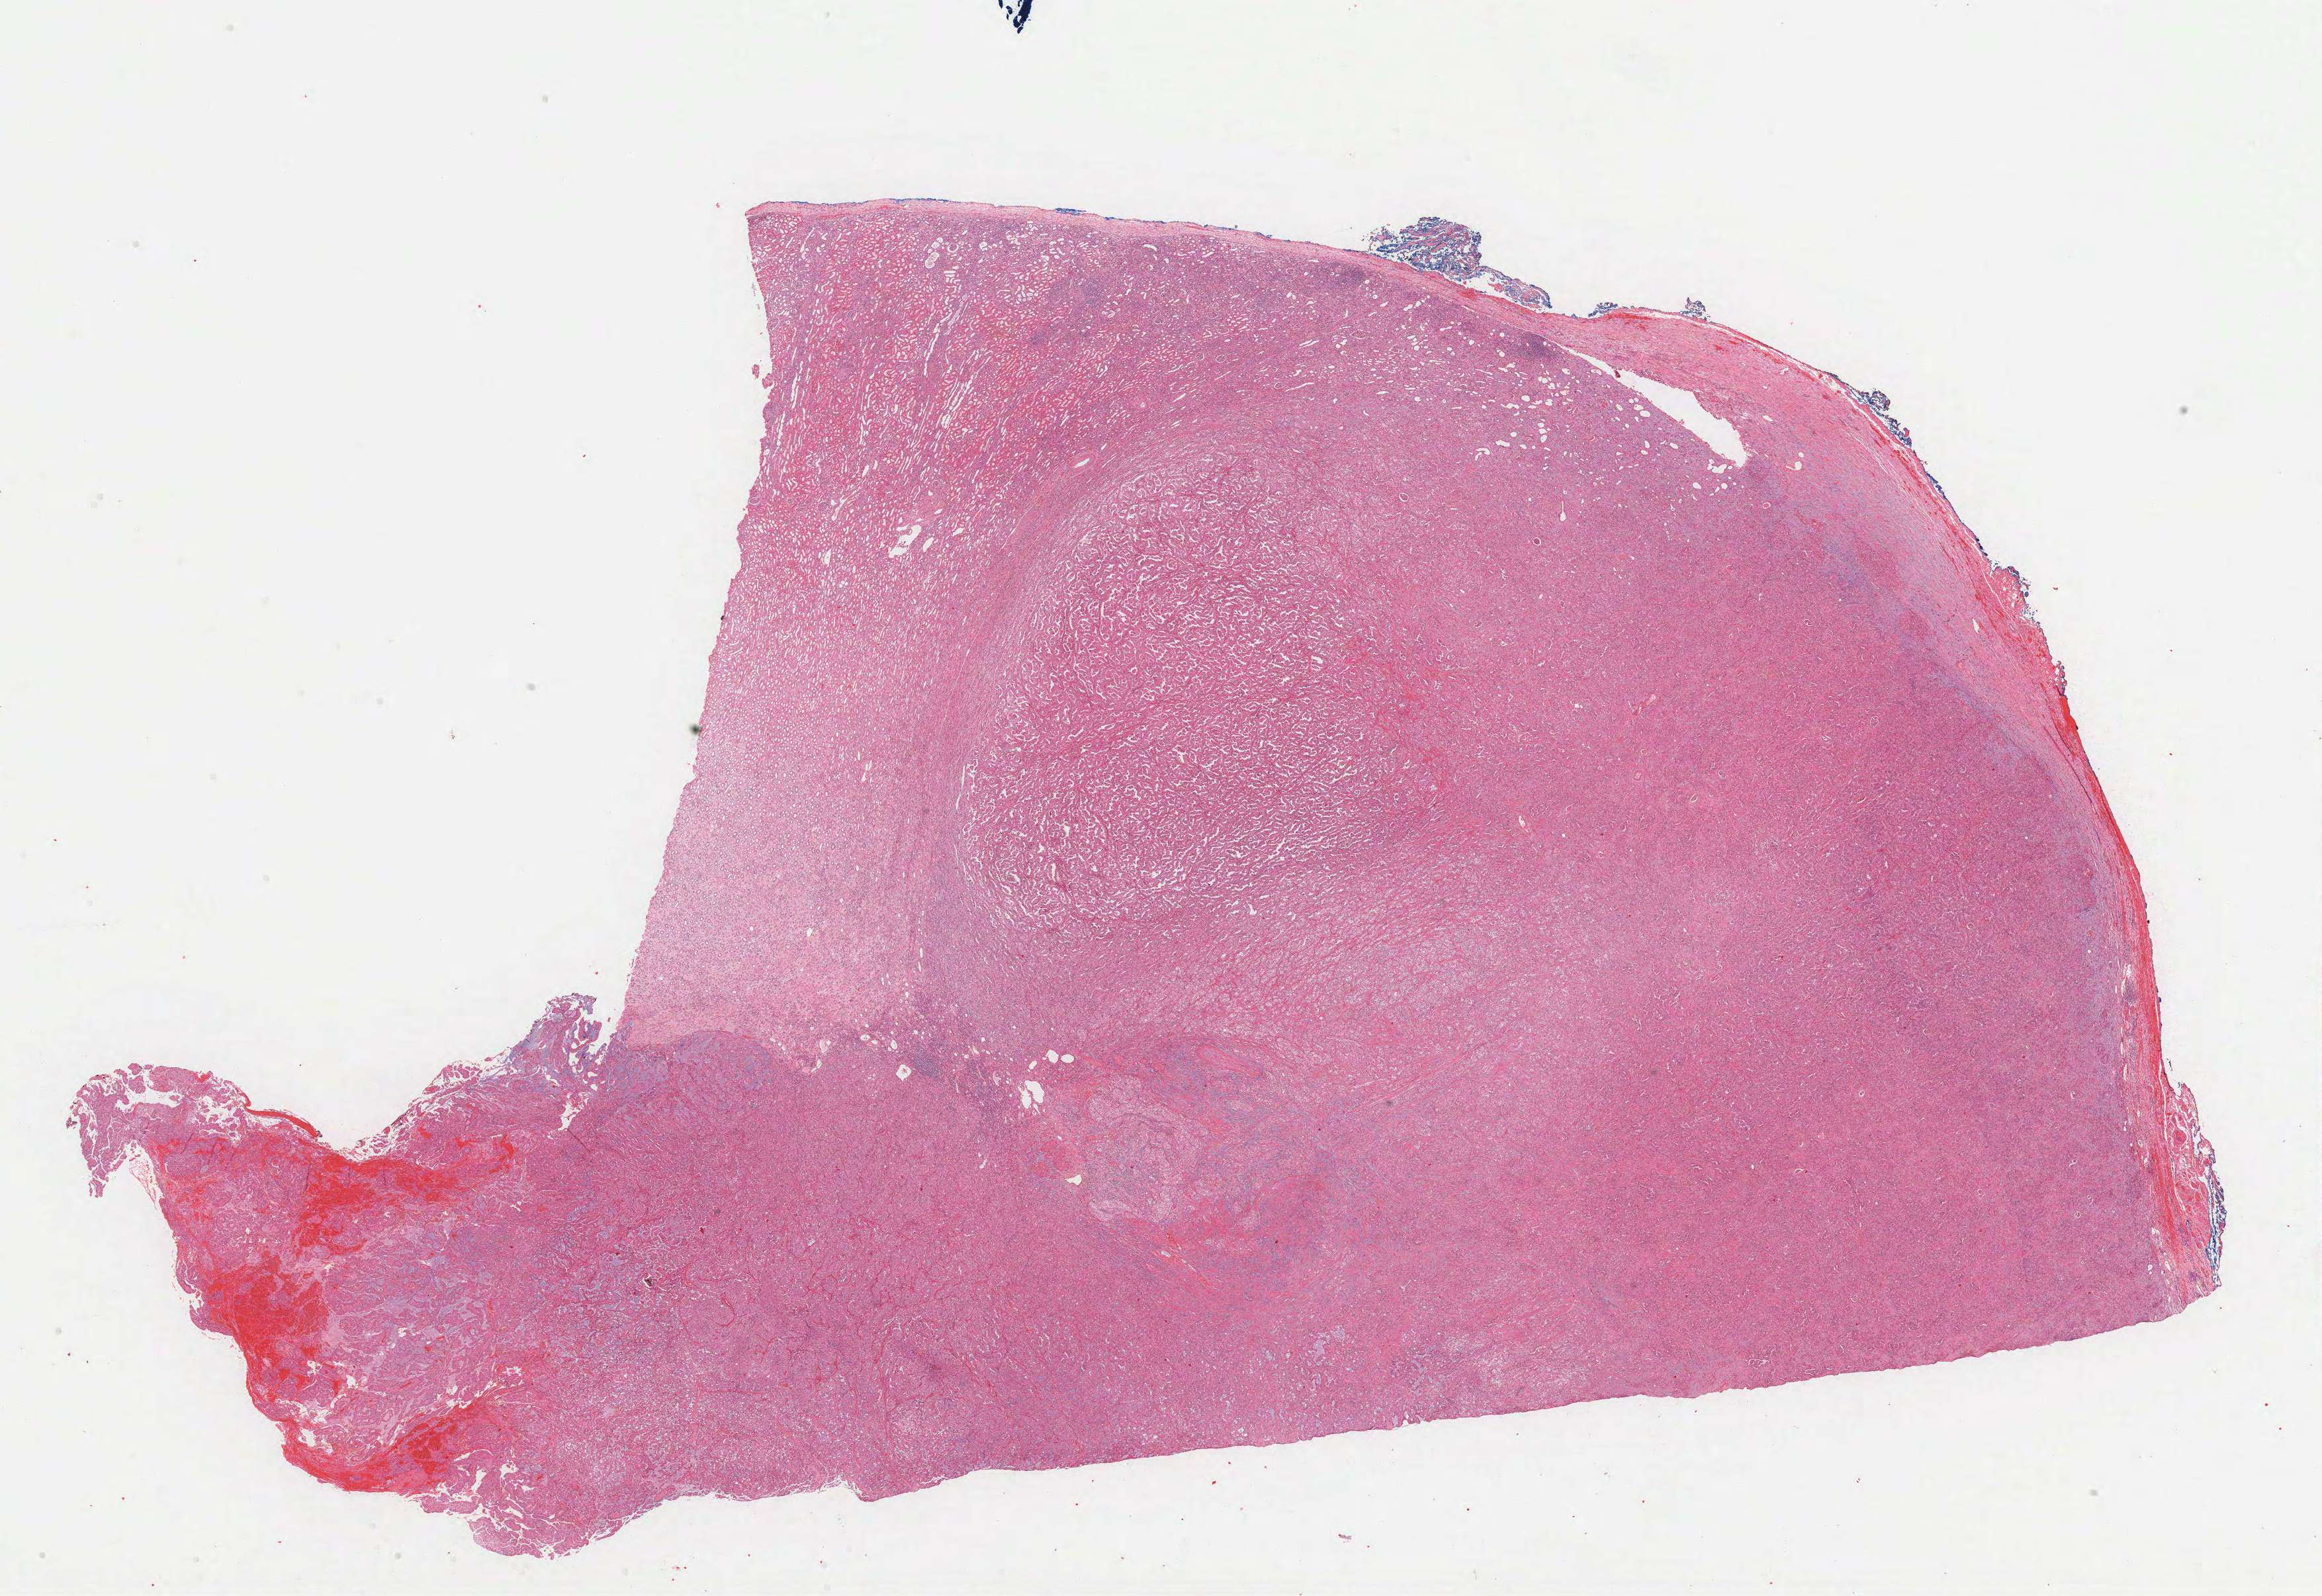
Digitized Hematoxylin and eosin (H&E) stained tissue section (whole slide), low-resolution overview of the scanned area, about 28.3 x 19.5 mm (from a 40x scan). FFPE section. Kidney, primary tumour sample. Patient: female, age at initial diagnosis 69 years.
TNM: T1a NX M0. AJCC pathologic stage: I (7th edition). Laterality: right. Histologic diagnosis: Papillary adenocarcinoma, NOS.